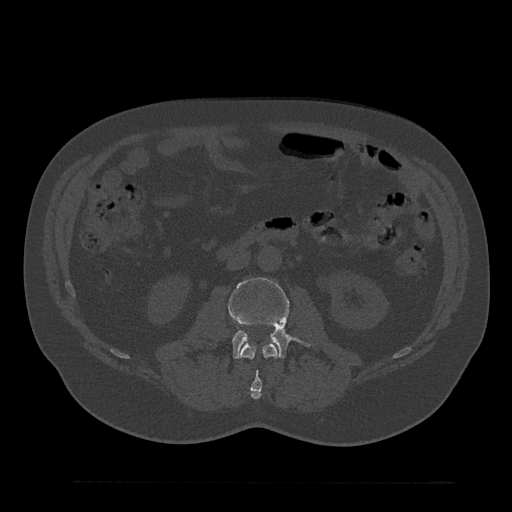
CT including the spine, one axial slice; position 60 of 797 along the scan axis; 120 kVp; bone window (W 1800 / L 400 HU); 512 × 512 image matrix, field of view 430 × 430 mm. Patient: male, 61 years. Case-level facts recorded for this patient, not image findings: primary cancer: prostate.
Structures marked on this image (semi-automatically segmented with operator editing):
- L2 vertebra: bounding box (x1, y1, x2, y2) in pixels: (240, 343, 278, 399)
- L3 vertebra: (228, 277, 309, 358)